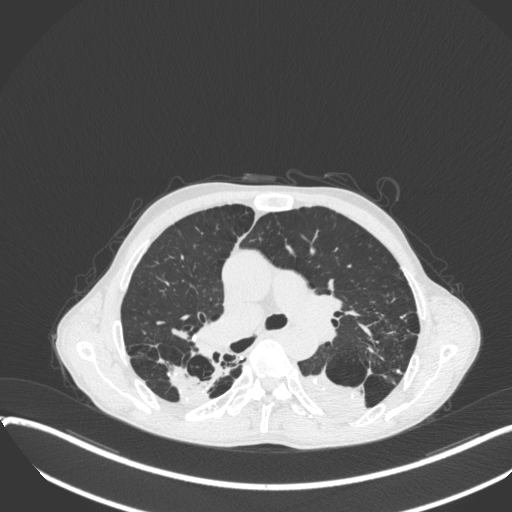
Chest CT, one axial slice. Position 241 of 400 along the scan axis. Reconstruction kernel B31f. Lung window (W 1500 / L -600 HU). 1 mm slice thickness. 512 × 512 image matrix. Patient: male, 57 years. From the clinical record (not read from this slice): clinical TNM (as recorded): T4 N0 M0.
Outlined on this slice (bounding box drawn by a radiologist):
- lung tumour (recorded histology: squamous cell carcinoma): bounding box [x1, y1, x2, y2] px = [296, 364, 365, 417]